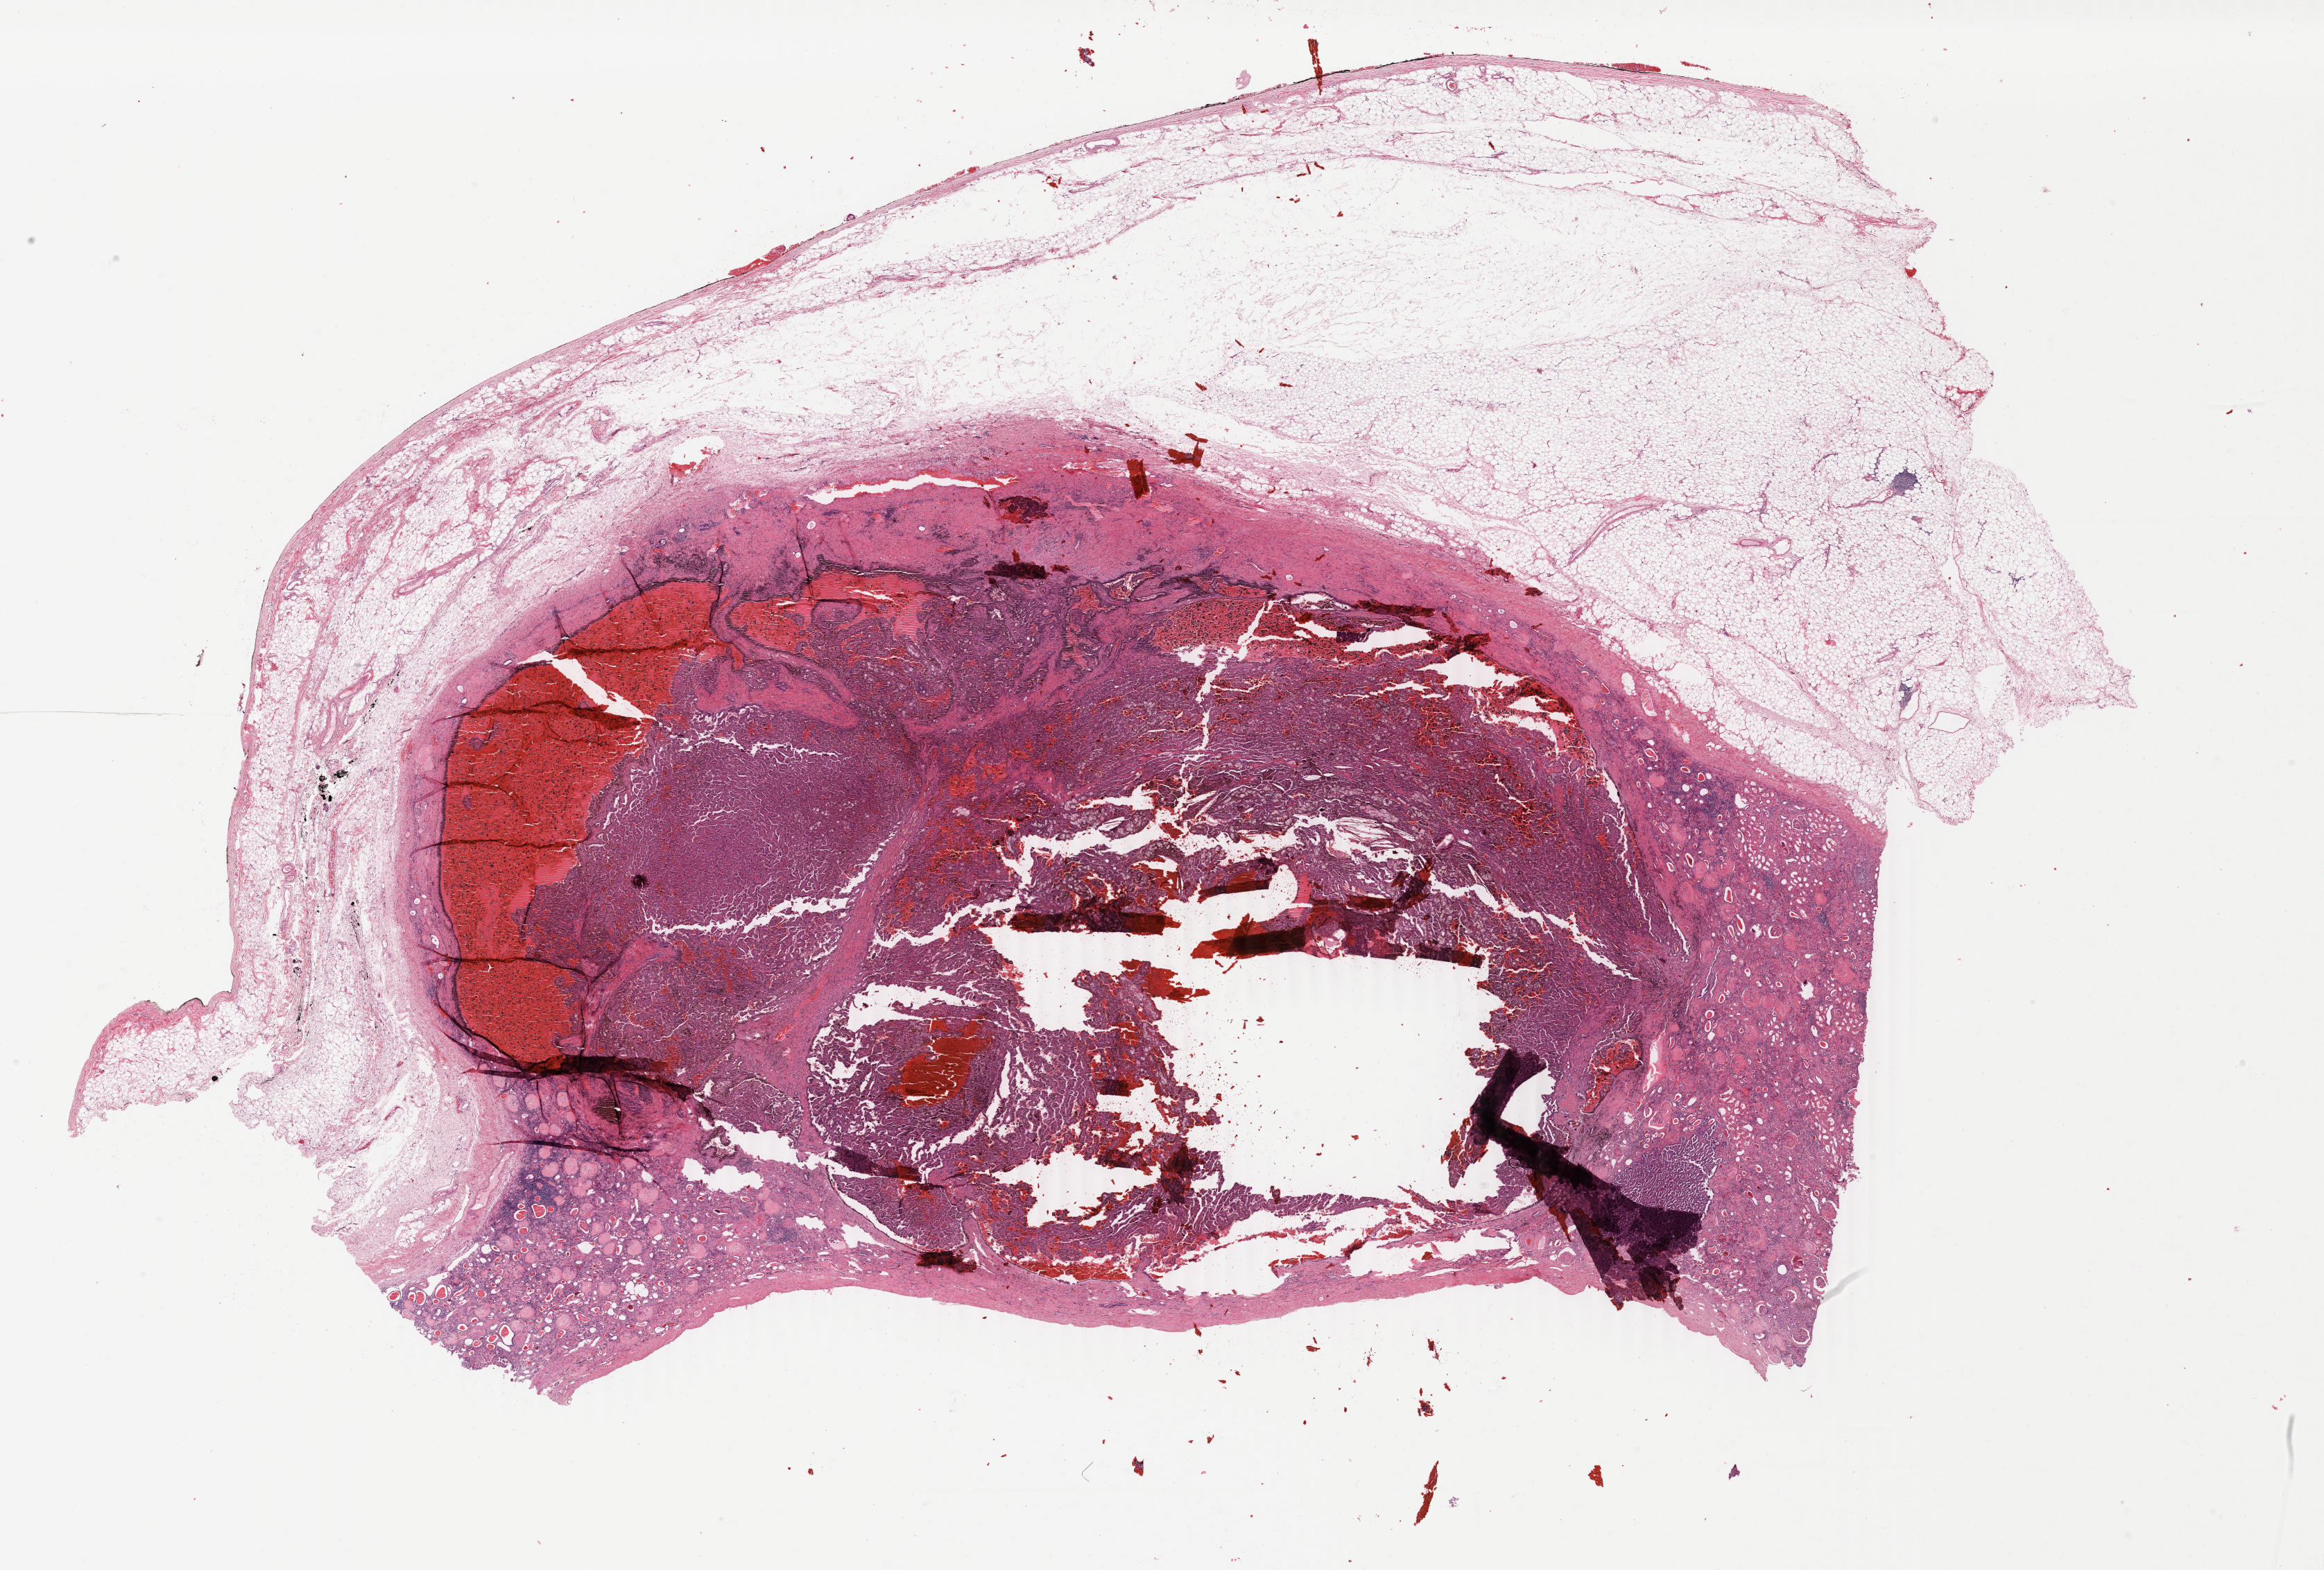
H&E whole-slide image, low-resolution overview of the scanned area, about 26.7 x 18.0 mm (from a 40x scan). FFPE section. Sample: primary tumour, kidney. Patient: male, age at initial diagnosis 69 years.
• laterality: right
• AJCC pathologic stage: I (7th edition)
• histologic diagnosis: Papillary adenocarcinoma, NOS